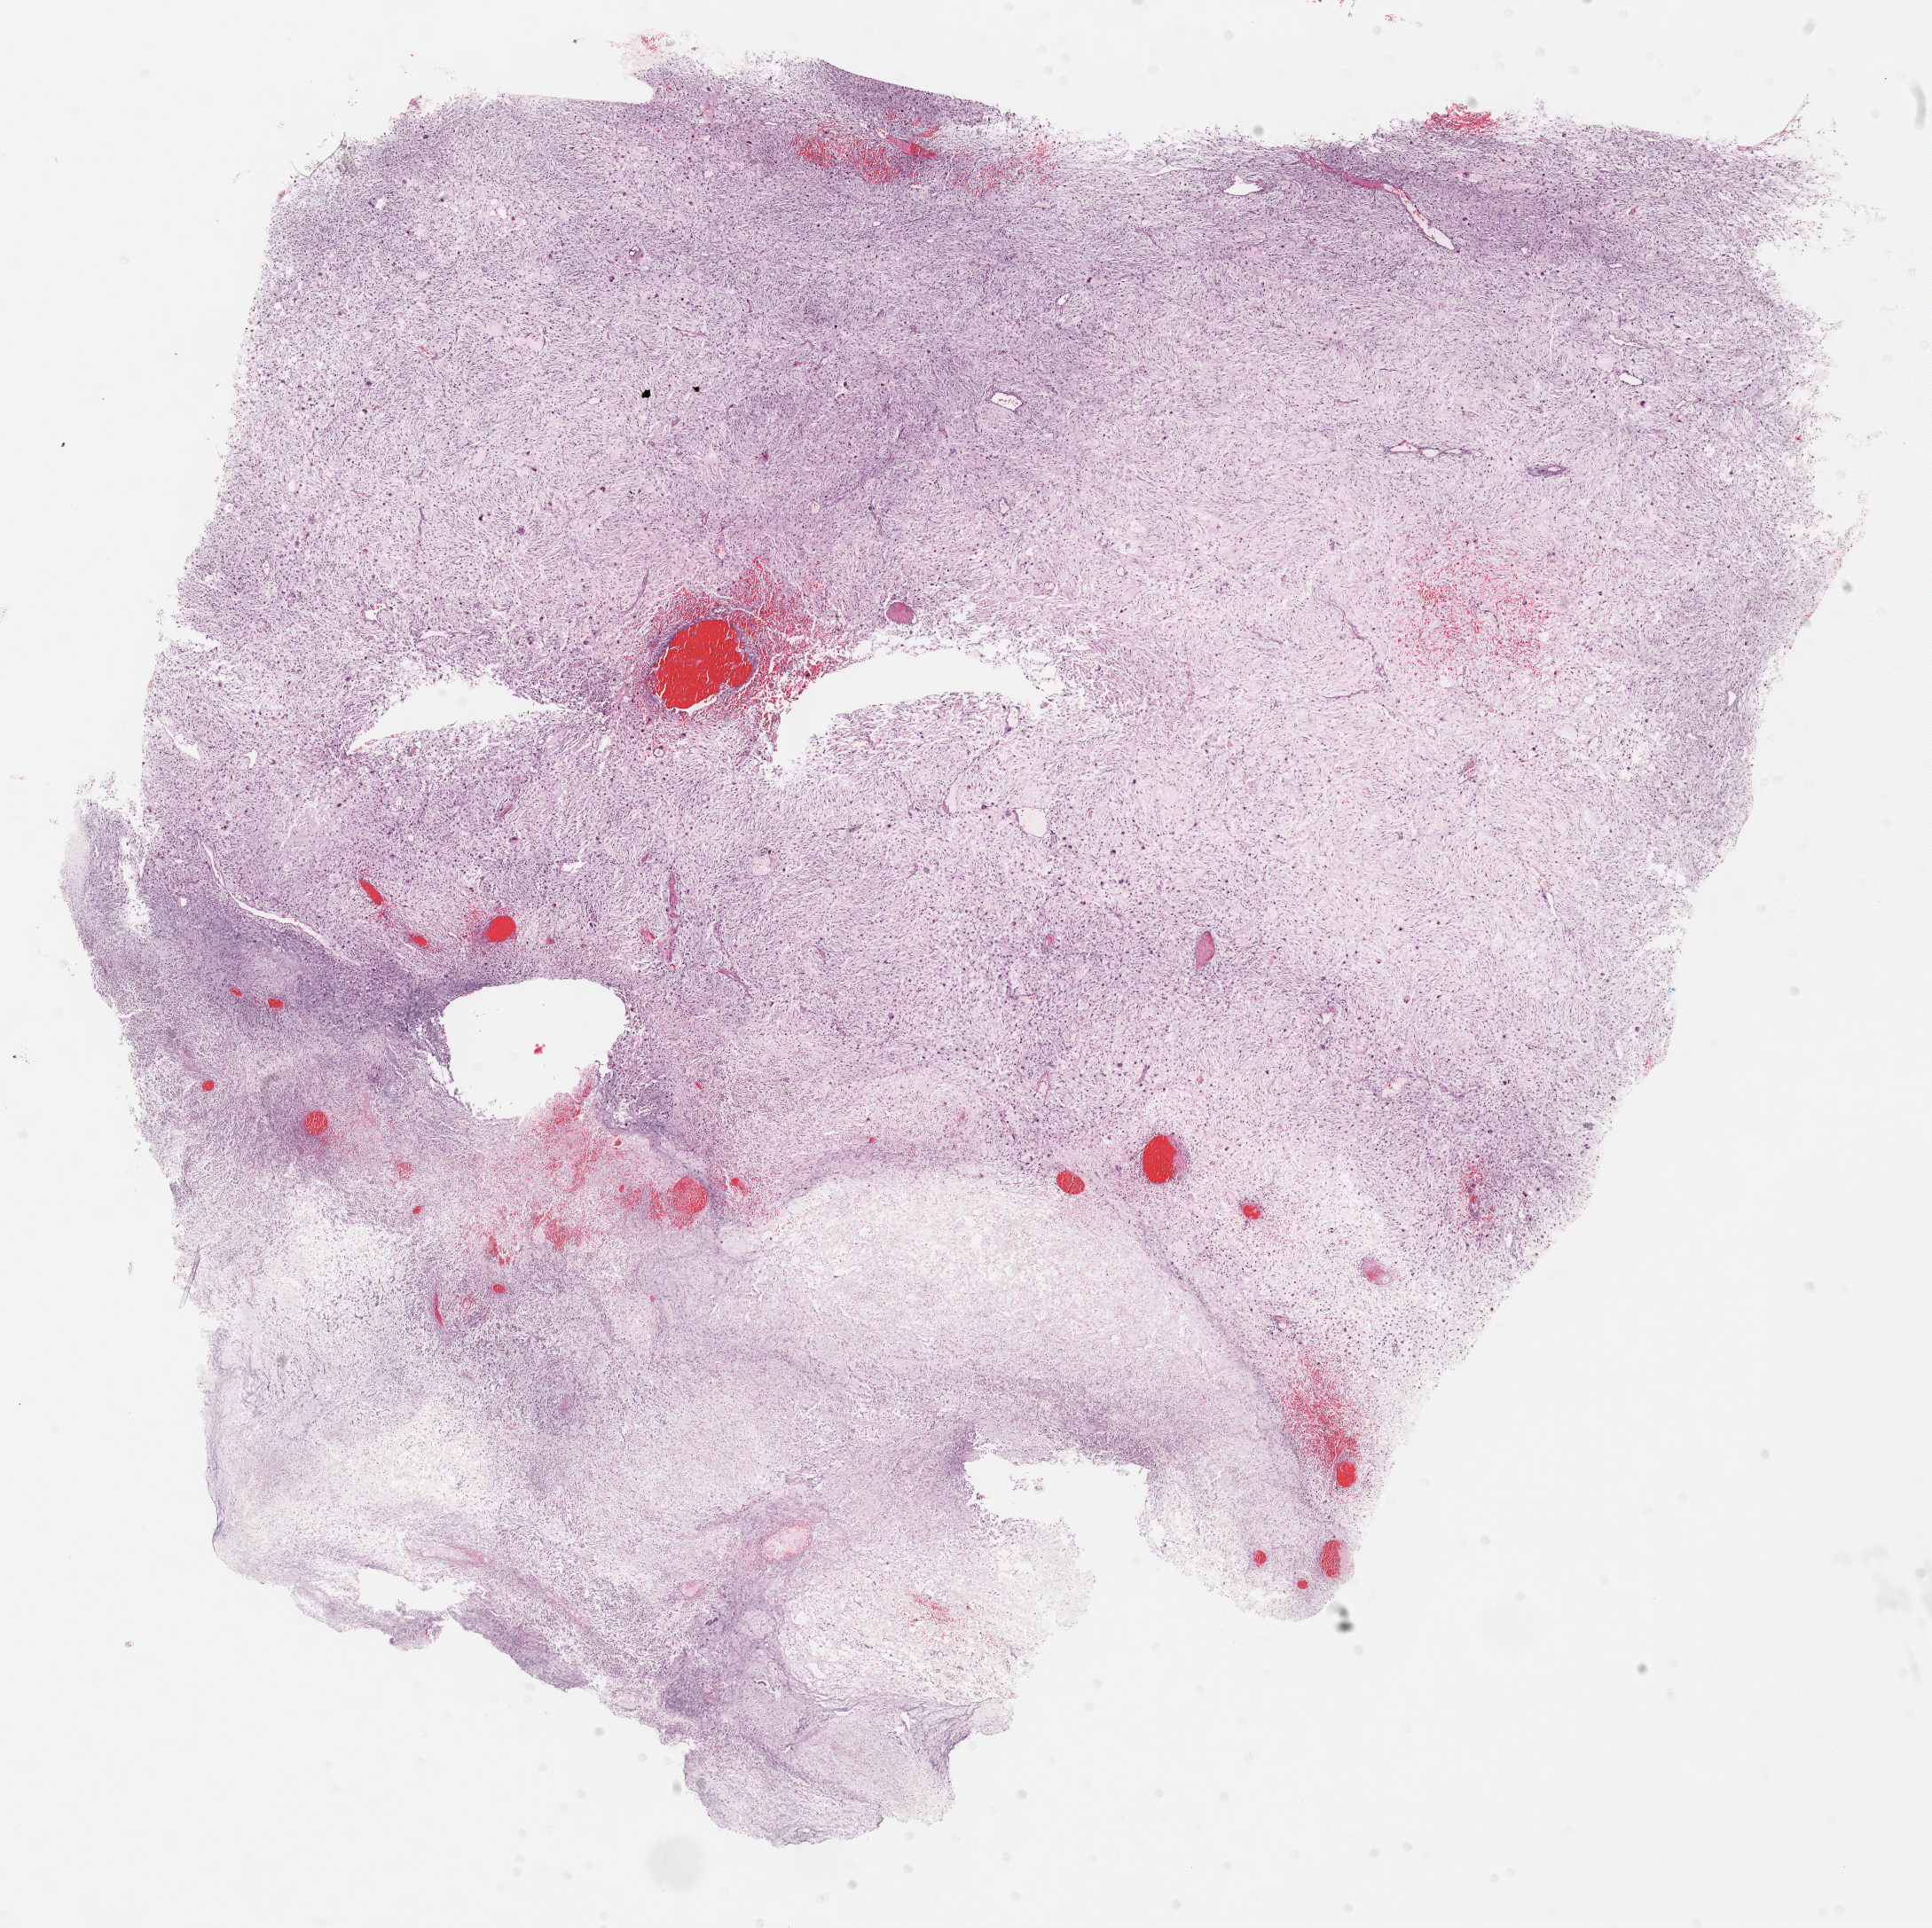
Hematoxylin and eosin (H&E) stained whole-slide image, low-resolution overview of the scanned area, about 17.6 x 17.6 mm. Formalin-fixed paraffin-embedded (FFPE) diagnostic section. Connective, subcutaneous and other soft tissues, primary tumour sample. Male patient; age at initial diagnosis 74 years.
- histologic diagnosis: Fibromyxosarcoma (connective, subcutaneous and other soft tissues of lower limb and hip)